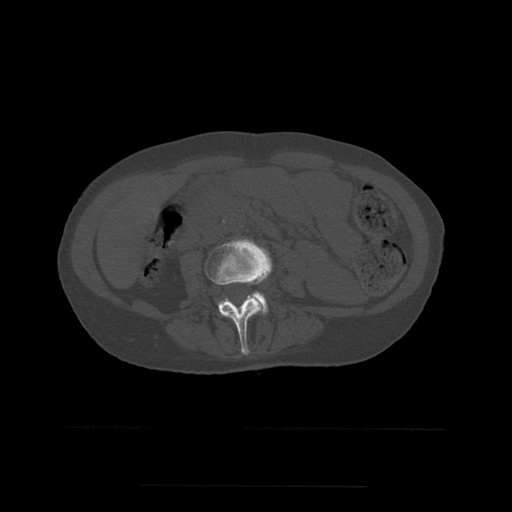
CT including the spine, one axial slice; position 183 of 544 along the scan axis; bone window (W 1800 / L 400 HU); 512 × 512 image matrix, field of view 350 × 350 mm. Patient age 58 years. Case-level facts recorded for this patient, not image findings: primary cancer: lung.
Annotated regions visible in this slice (semi-automatically segmented with operator editing):
- L3 vertebra: bounding box (x1, y1, x2, y2) in pixels: (204, 239, 272, 355)
- L4 vertebra: (218, 292, 268, 315)